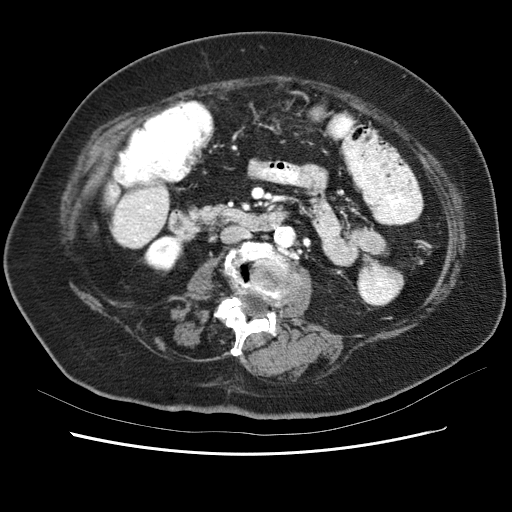
Contrast-enhanced abdominal CT (liver protocol), one axial slice. Slice 9 of 62 in the series (ordered by position). Reconstruction kernel STANDARD. Soft-tissue window (W 400 / L 40 HU). 512 × 512 image matrix, field of view 340 × 340 mm. From the clinical record (not read from this slice): diagnosis: hepatocellular carcinoma (patient treated with transarterial chemoembolisation; whether this scan precedes or follows treatment is not stated here); TNM stage (as recorded): Stage-I; Child-Pugh class: B; tumour nodularity: uninodular; tumour size: 5.3 cm.
Annotated regions visible in this slice (semi-automatic segmentation, software-assisted and operator-edited):
- liver parenchyma outside the tumour (the mass and vessels are separate outlines, so this box may not span the whole liver): bounding box [x1, y1, x2, y2] px = [108, 182, 170, 249]
- liver vessels: [125, 188, 164, 242]